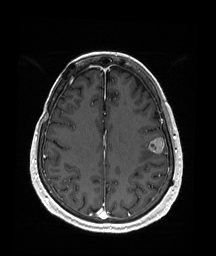
Brain MRI from a brain-tumour surgery series, one axial slice. T1-weighted post-contrast. 1 mm slice thickness. 216 × 256 image matrix, field of view 211 × 250 mm. Case-level facts recorded for this patient, not image findings: histopathology: Metastatic Malignant Melanoma.
Structures marked on this image (expert manual segmentation):
- tumour: bounding box [x1, y1, x2, y2] px = [148, 137, 165, 153]